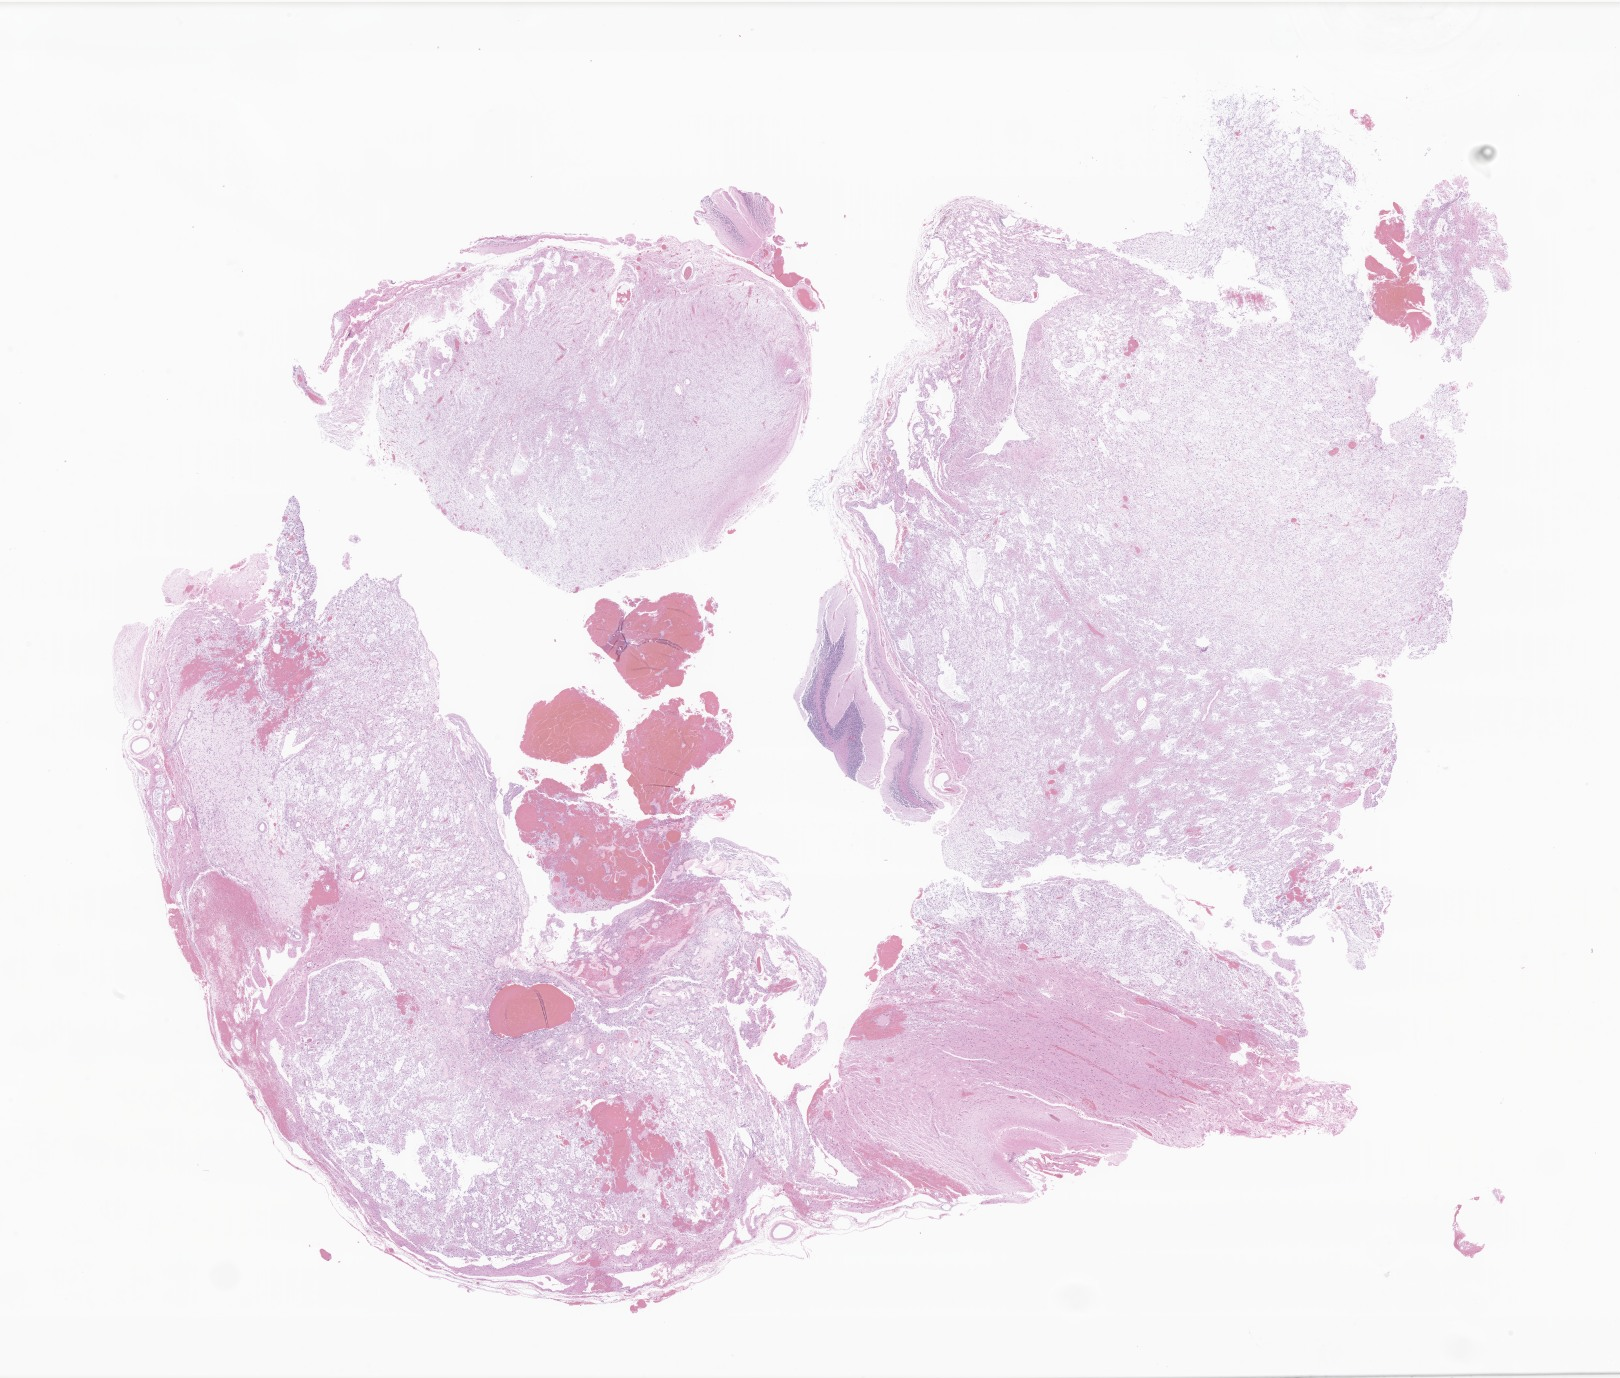
Whole-slide image, H&E stain of tumor tissue from the brain — low-resolution overview of the scanned area, about 27.3 x 23.2 mm, formalin-fixed paraffin-embedded section. Patient male; age 162 months (13 years 6 months).
* recorded diagnosis: Pilocytic astrocytoma